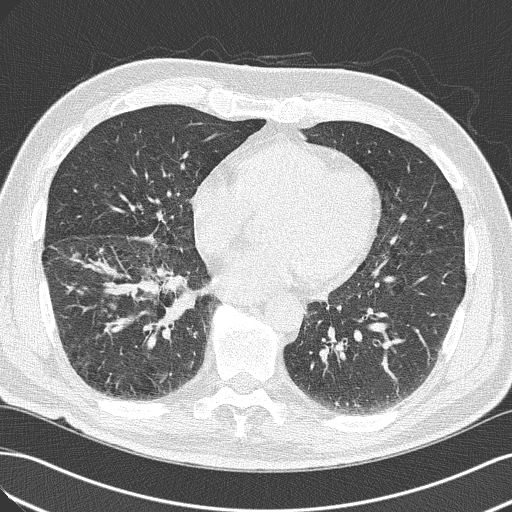
Low-dose screening chest CT, axial slice. Baseline annual screen. Lung window (W 1500 / L -600 HU). Slice 96 of 143 in the series. Male, age 65 years at enrolment. Current smoker at enrolment.
Expert reader's lesion annotation, bounding box <104,243,202,338> (left, top, right, bottom; pixels). The exam's reader record, not a measurement of the box and not confirmed to be the same lesion: non-calcified nodule or mass ≥4 mm, right upper lobe, 18 × 13 mm, spiculated (stellate) margins, soft tissue attenuation. Official screen result: positive, change unspecified: nodule(s) >= 4 mm or enlarging nodule(s), mass(es), or other non-specific abnormalities suspicious for lung cancer. Later outcome: lung cancer diagnosed 14 days after this screen — adenocarcinoma, NOS, right lower lobe, poorly differentiated (G3), stage IIIA (AJCC 6th edition), 40 mm at pathology.